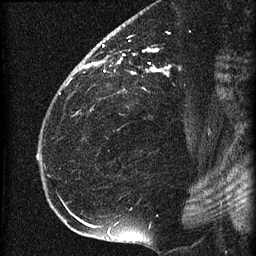
Breast MRI (dynamic contrast-enhanced), one sagittal slice; dynamic contrast-enhanced series, image 2 of 4 at this slice position (ordered by acquisition); 1.5 T; TE 4.2 ms, TR 22.7 ms; 1.5 mm slice thickness; 256 × 256 image matrix. Female patient, age 35 years. From the clinical record (not read from this slice): setting: breast cancer imaged before/during neoadjuvant chemotherapy; receptor status: HR-positive, HER2-negative.
Annotated regions visible in this slice (semi-automatic segmentation, software-assisted and operator-edited):
- analysis volume of interest (the breast-tissue region the enhancement analysis was run in; not a lesion): box from (x=69, y=27) to (x=198, y=112) px
- tumour enhancement mask (voxels above the 90 % enhancement threshold inside the analysis volume of interest): (x=79, y=45)–(x=168, y=111)